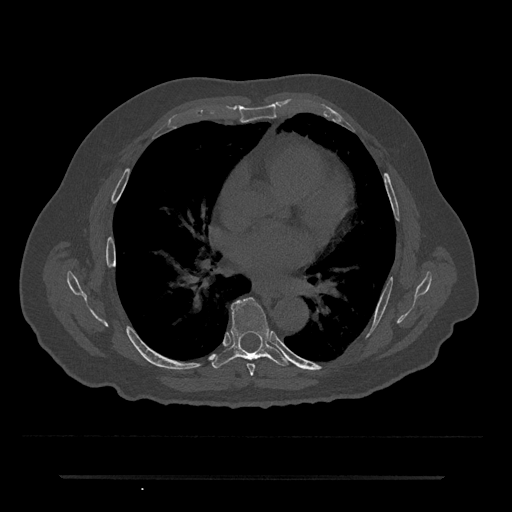
CT including the spine, one axial slice. Position 400 of 797 along the scan axis. Reconstruction kernel Br40s/3. Bone window (W 1800 / L 400 HU). 0.5 mm slice thickness. 512 × 512 image matrix. Patient: male, 69 years. From the clinical record (not read from this slice): primary cancer: prostate.
Structures marked on this image (semi-automatically segmented with operator editing):
- T6 vertebra: bounding box (x1, y1, x2, y2) in pixels: (247, 363, 255, 375)
- T7 vertebra: (212, 297, 289, 369)